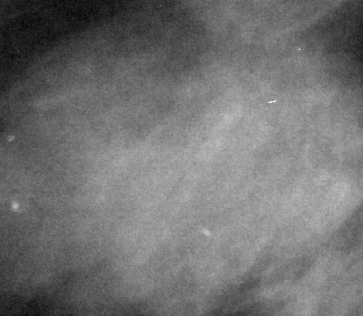
Crop from a digitized film mammogram around one marked abnormality, right breast, MLO view.
Mass, shape lobulated, margins circumscribed; BI-RADS assessment category 3; subtlety rating 5 on a 1 (subtle) to 5 (obvious) scale; pathology (as recorded): benign.